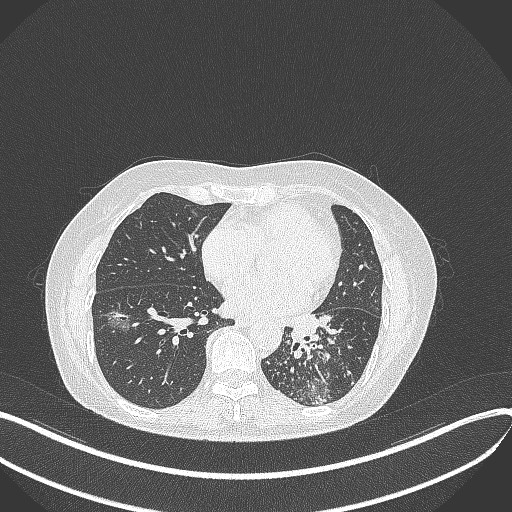
Chest CT, one axial slice; position 166 of 429 along the scan axis; reconstruction kernel B70f; 100 kVp; lung window (W 1500 / L -600 HU); 1 mm slice thickness; 512 × 512 image matrix. Patient: female, 63 years. From the clinical record (not read from this slice): clinical TNM (as recorded): T1b N0 M0.
Structures marked on this image (rectangle marked by the reading radiologist):
- lung tumour (recorded histology: adenocarcinoma): bounding box (x1, y1, x2, y2) in pixels: (282, 311, 324, 345)